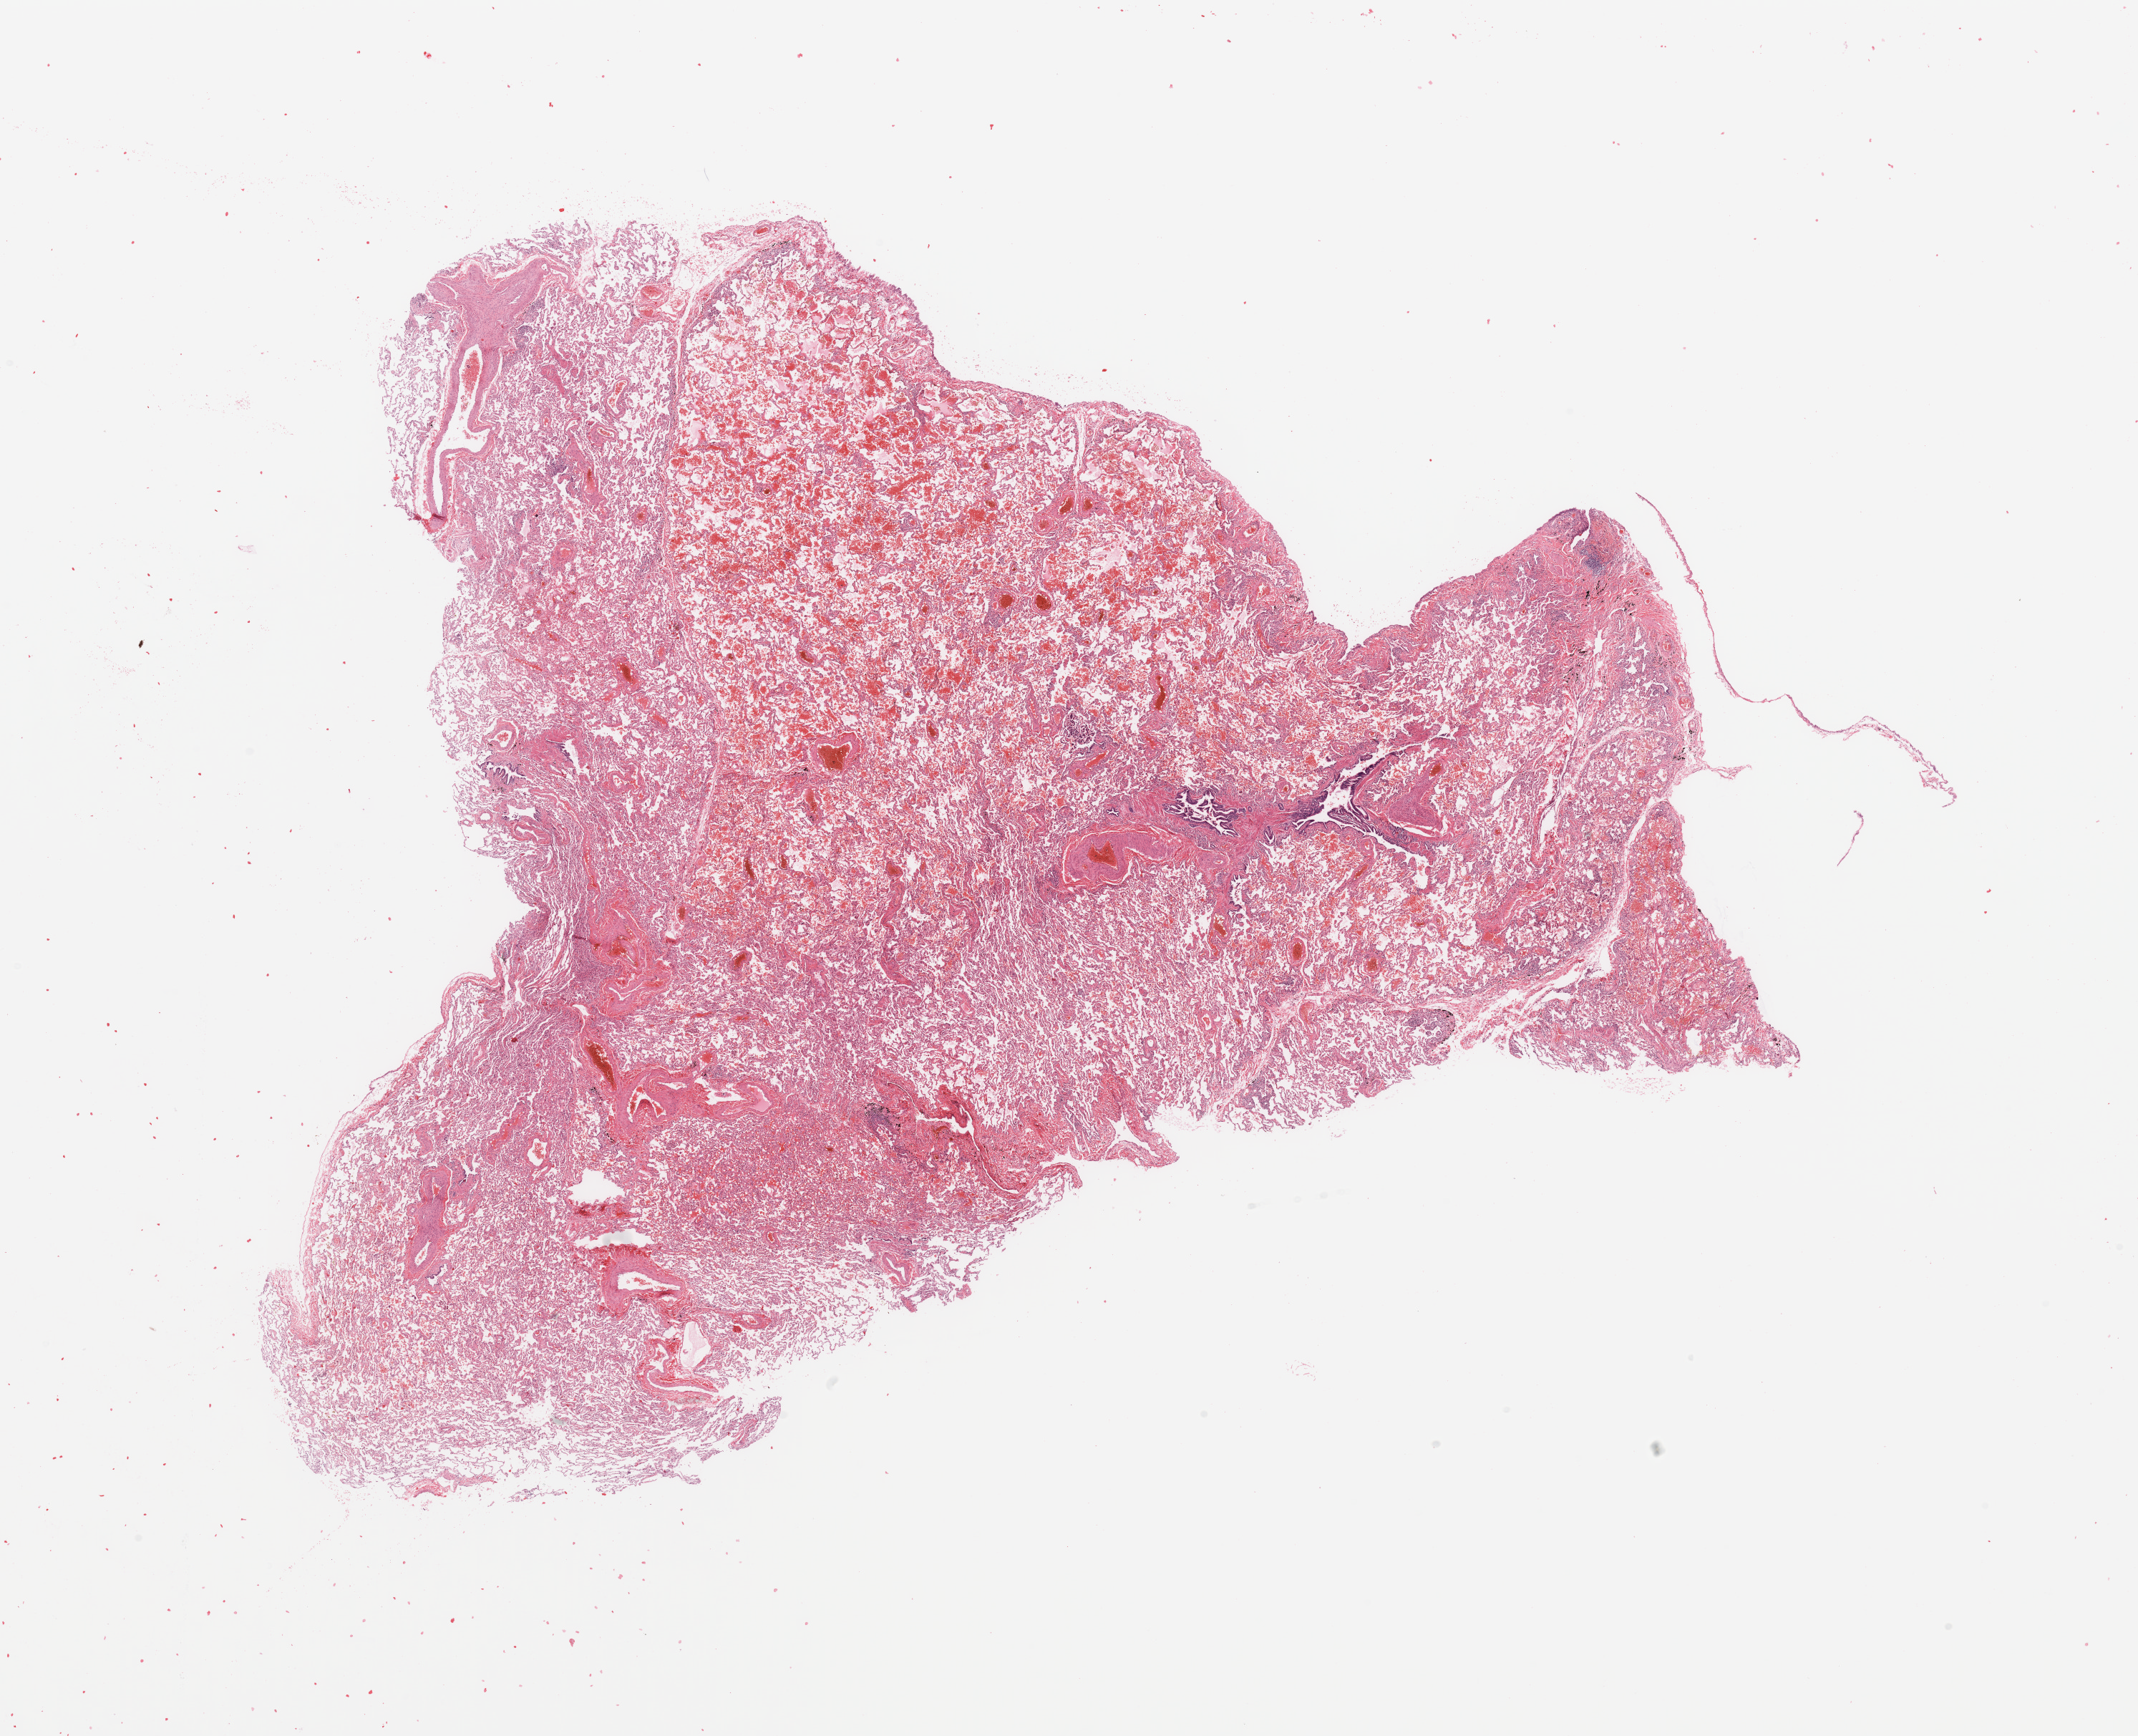
Digitized H&E-stained tissue section (whole slide) — a low-resolution overview of the entire scanned area, about 23.6 x 19.2 mm (acquisition: 20x scan), normal (non-tumour) tissue sample, lung. Male, 58 y/o.
- this section: normal (non-tumour) tissue from the same patient
- patient diagnosis: Adenocarcinoma, NOS